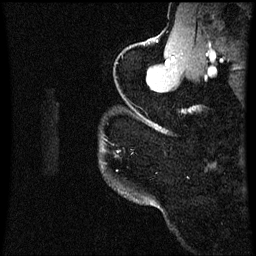
Breast MRI (dynamic contrast-enhanced), one sagittal slice. Slice 55 of 60 in the series (ordered by position). Dynamic contrast-enhanced series, image 2 of 3 at this slice position (ordered by acquisition). 1.5 T. TE 4.2 ms, TR 8.9 ms. 256 × 256 image matrix, field of view 200 × 200 mm. Patient: female, 58 years. From the clinical record (not read from this slice): setting: breast cancer imaged before/during neoadjuvant chemotherapy; receptor status: triple-negative.
Annotated regions visible in this slice (semi-automatic segmentation, software-assisted and operator-edited):
- analysis volume of interest (the breast-tissue region the enhancement analysis was run in; not a lesion): bounding box <104,118,167,153> (left, top, right, bottom; pixels)
- tumour enhancement mask (voxels above the 70 % enhancement threshold inside the analysis volume of interest): <156,124,161,129>